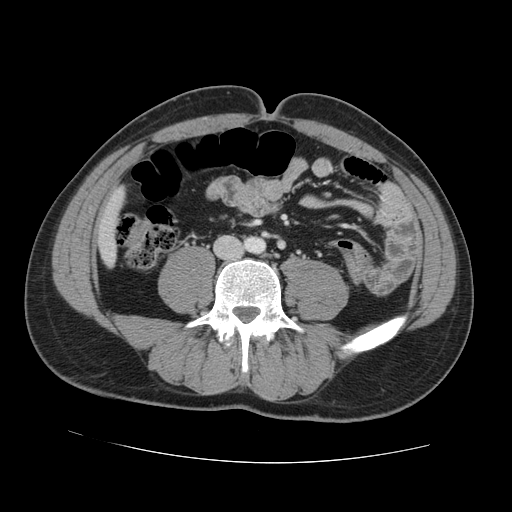
Contrast-enhanced abdominal CT, one axial slice. Position 11 of 131 along the scan axis. Intravenous contrast given. Soft-tissue window (W 400 / L 40 HU). 512 × 512 image matrix, field of view 380 × 380 mm. Male patient, age 40 years. Case-level facts recorded for this patient, not image findings: diagnosis: colorectal cancer liver metastases, imaged before liver resection; multiple liver metastases: yes; largest metastasis: 2.9 cm; disease in both lobes: yes.
Outlined on this slice (manually delineated by an expert):
- liver: box from (x=99, y=193) to (x=123, y=263) px